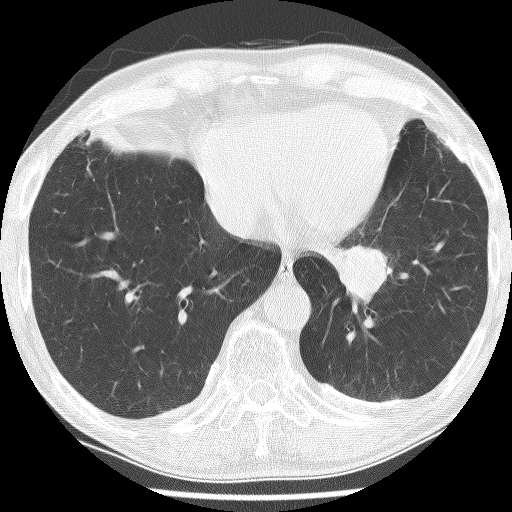
Low-dose screening chest CT, one axial slice; position 50 of 226 along the scan axis; reconstruction kernel BONE; lung window (W 1500 / L -600 HU); 512 × 512 image matrix, field of view 320 × 320 mm.
Structures marked on this image (manually delineated by an expert):
- lesion 1 (tumor, lower lobe of left lung): bounding box [x1, y1, x2, y2] px = [339, 244, 389, 304]